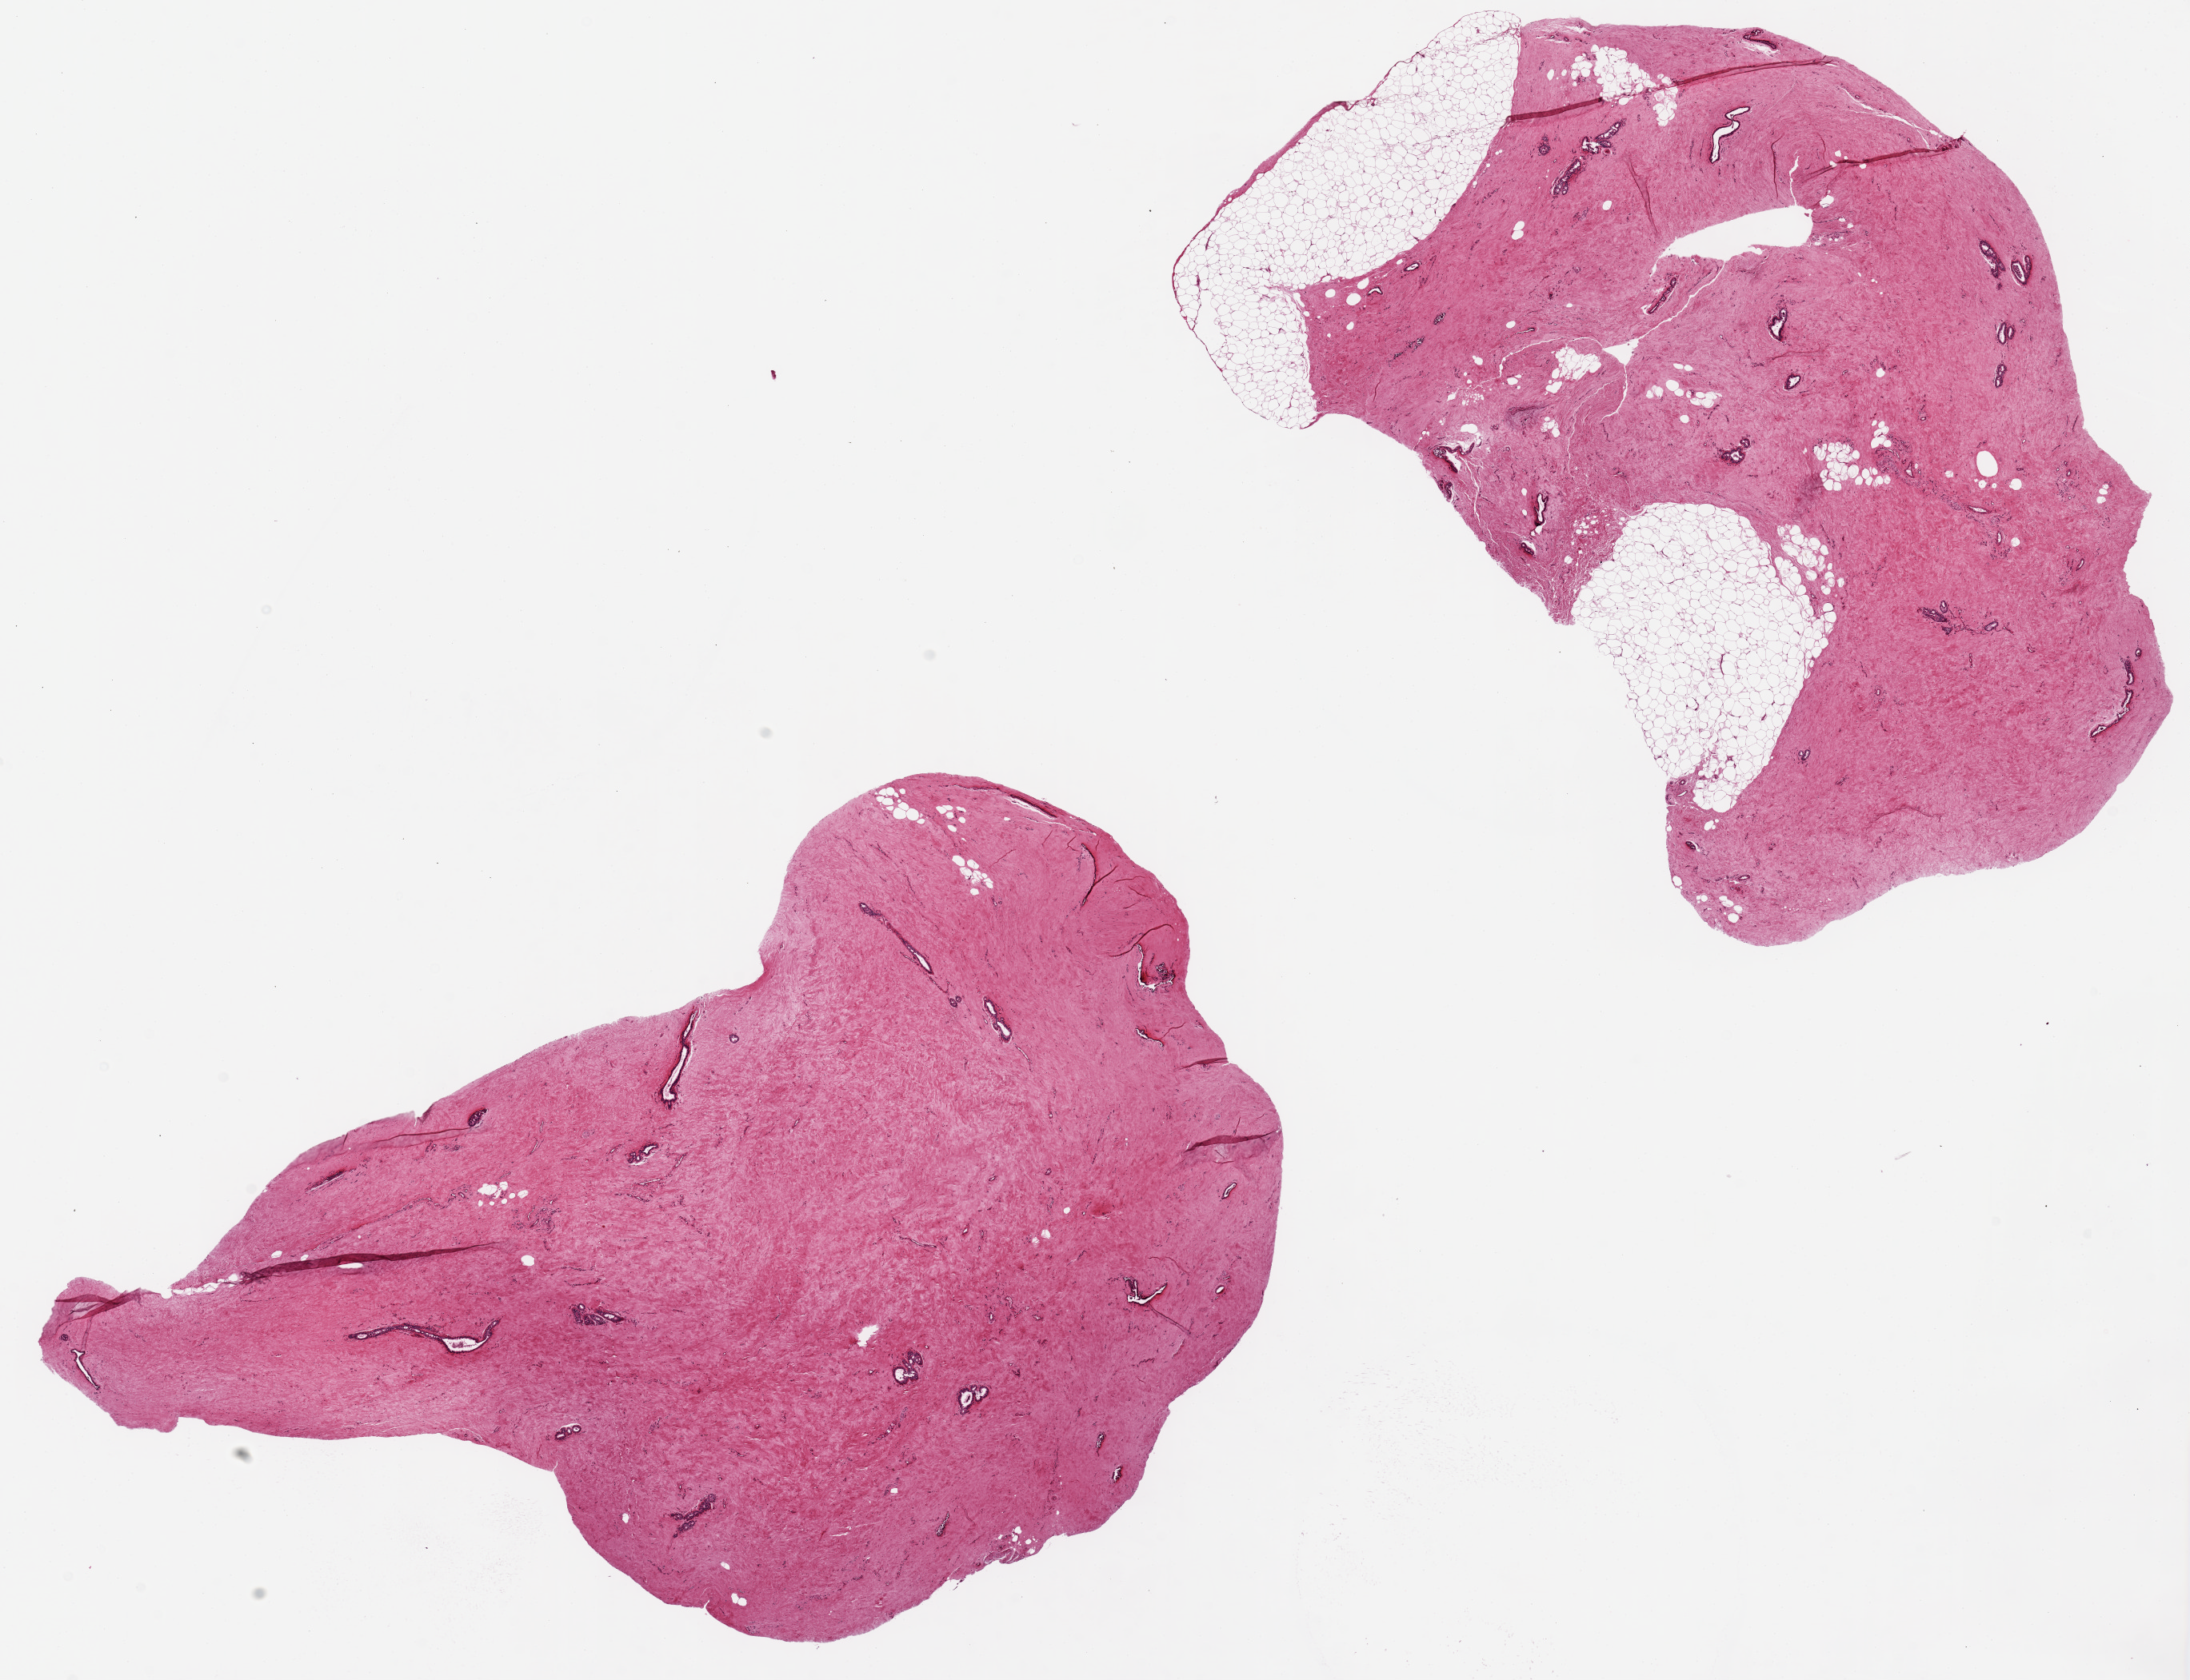
Digitized haematoxylin and eosin-stained section, low-resolution overview of the scanned area, about 21.7 x 16.6 mm. PAXgene-fixed, paraffin-embedded tissue. Target tissue: breast. Tissue donor sample.
- pathologist's review note for this sample: 2 pieces, 12x7 & 10x6mm; gynecomastia: fibrosis and ducts